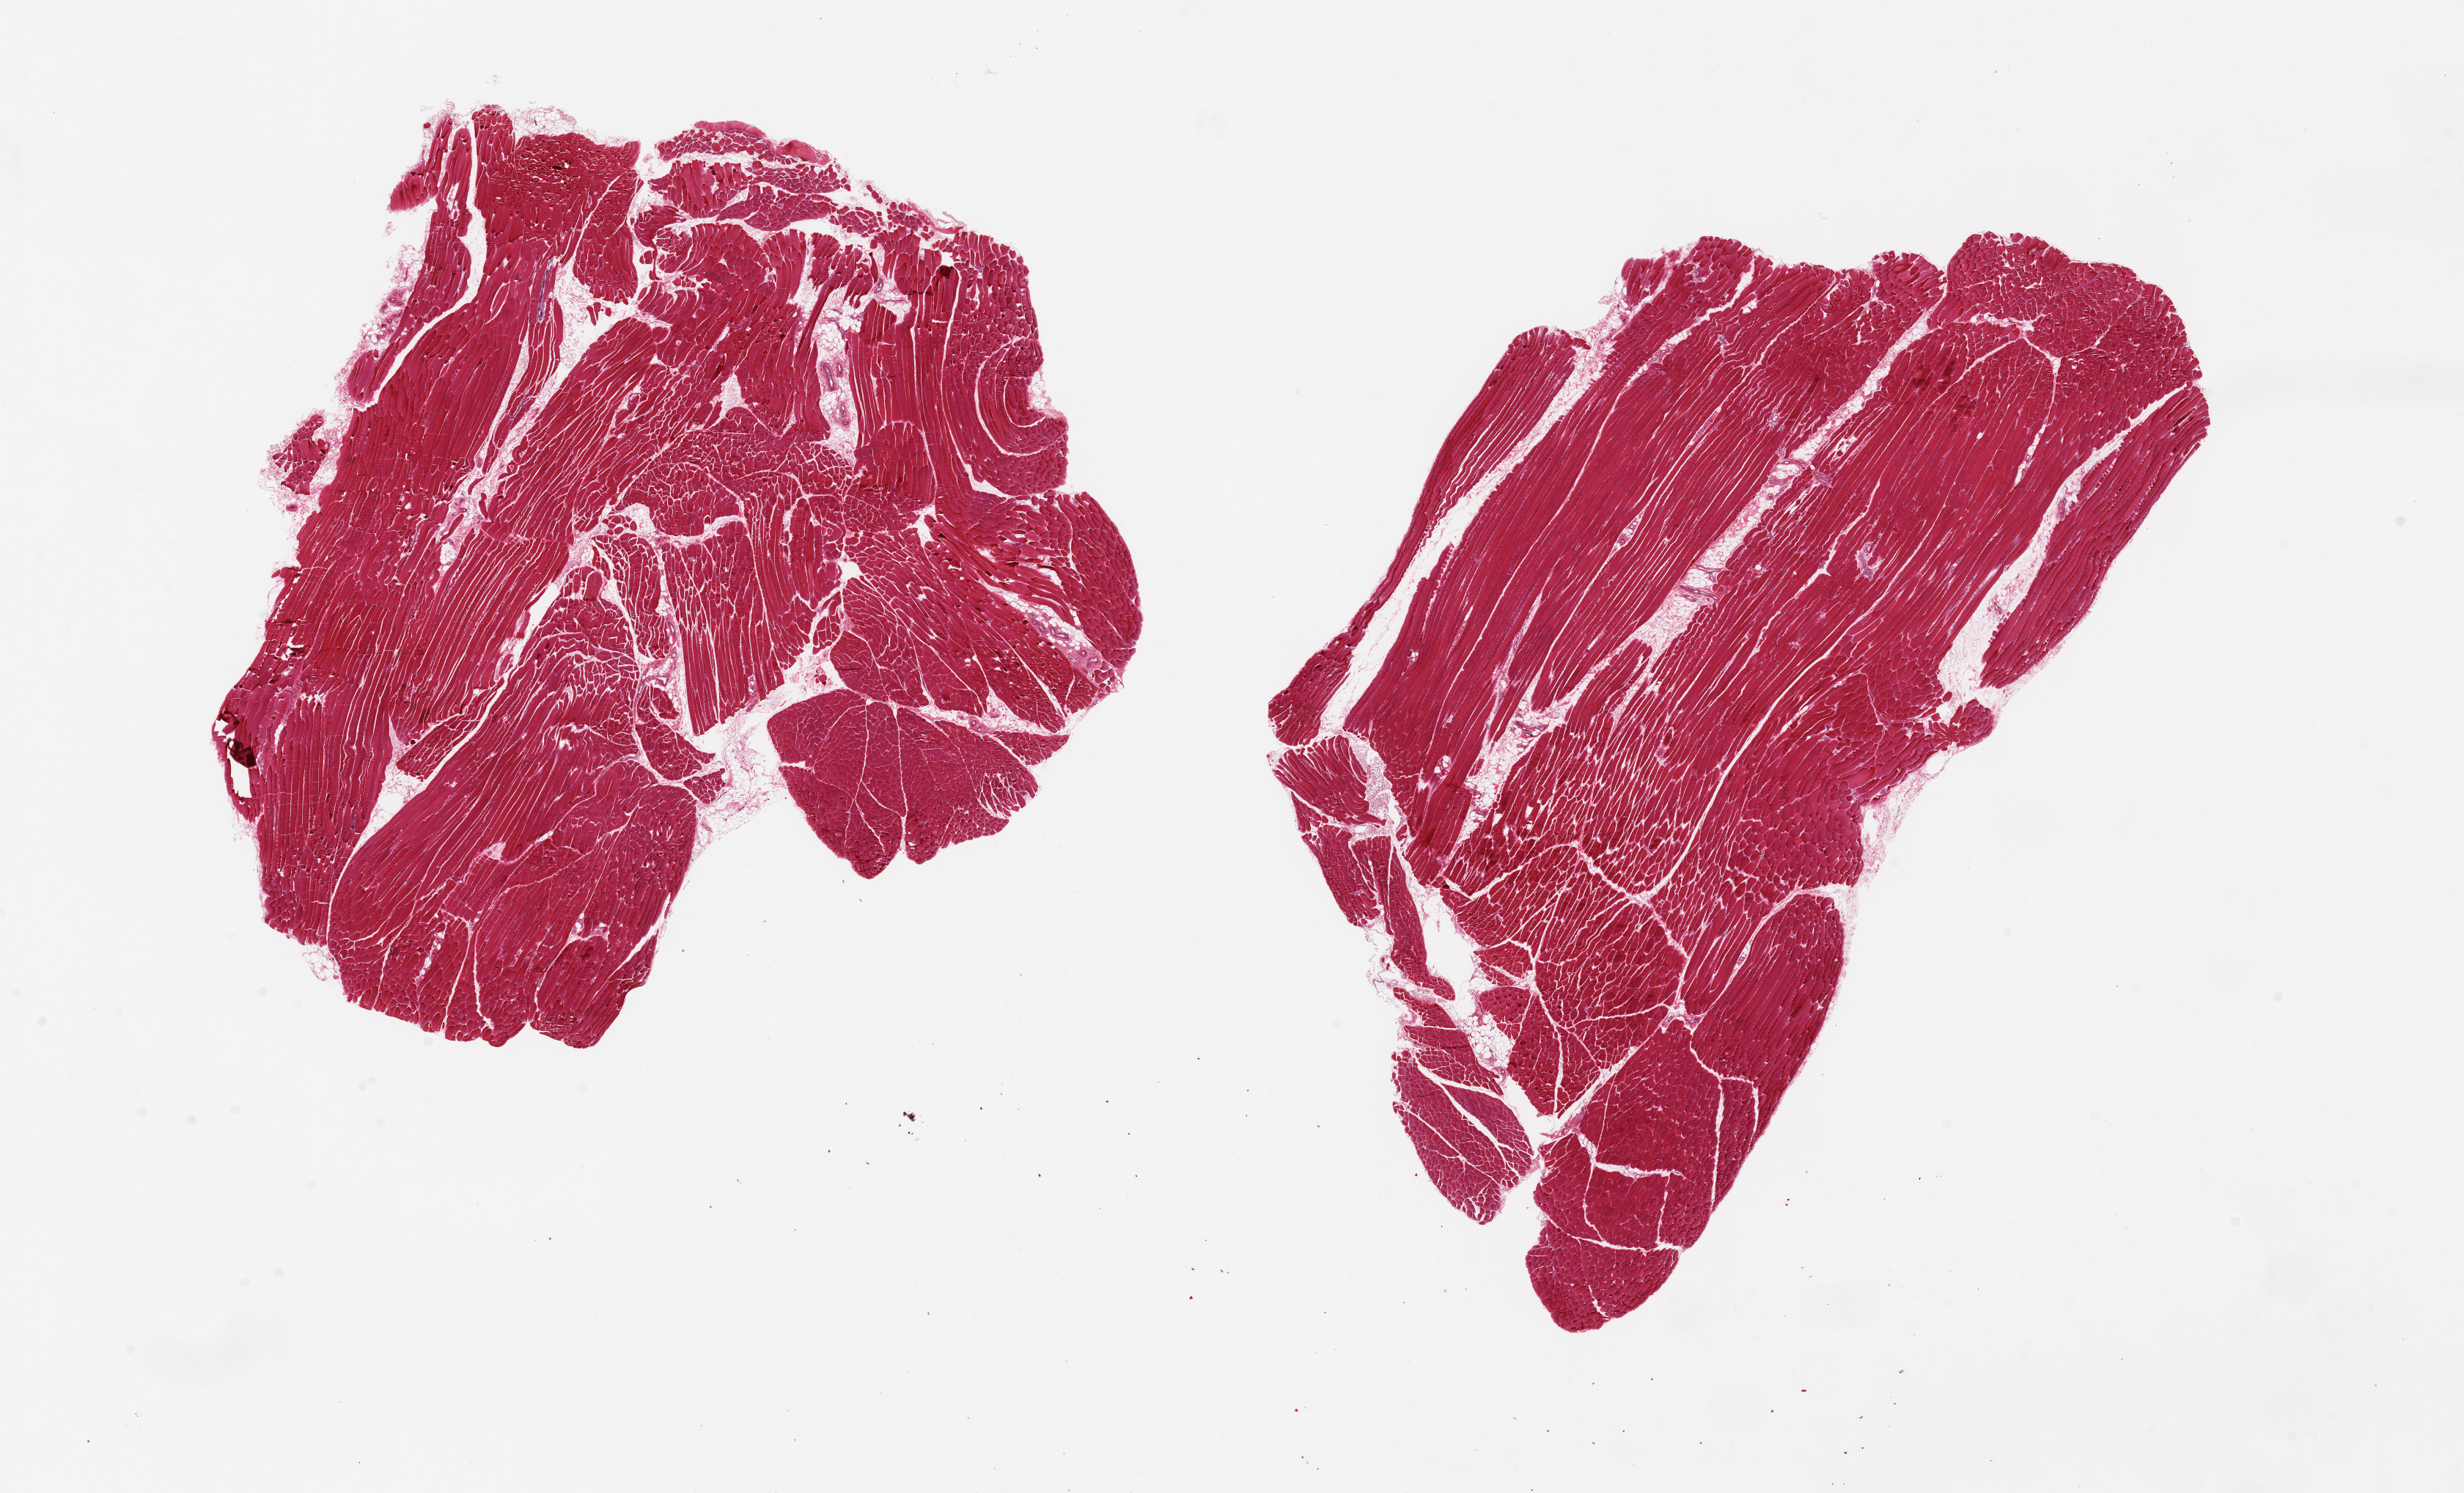
Whole-slide image, H&E stain, shown as a low-resolution overview of the whole scanned area (about 26.6 x 16.1 mm), PAXgene-fixed paraffin-embedded (PFPE) section, sampled site (target tissue): skeletal muscle, tissue donor sample. Female donor.
Pathologist's review note for this sample: 2 pieces, 10x10 & 13x8mm; ~10% interstitial fat.